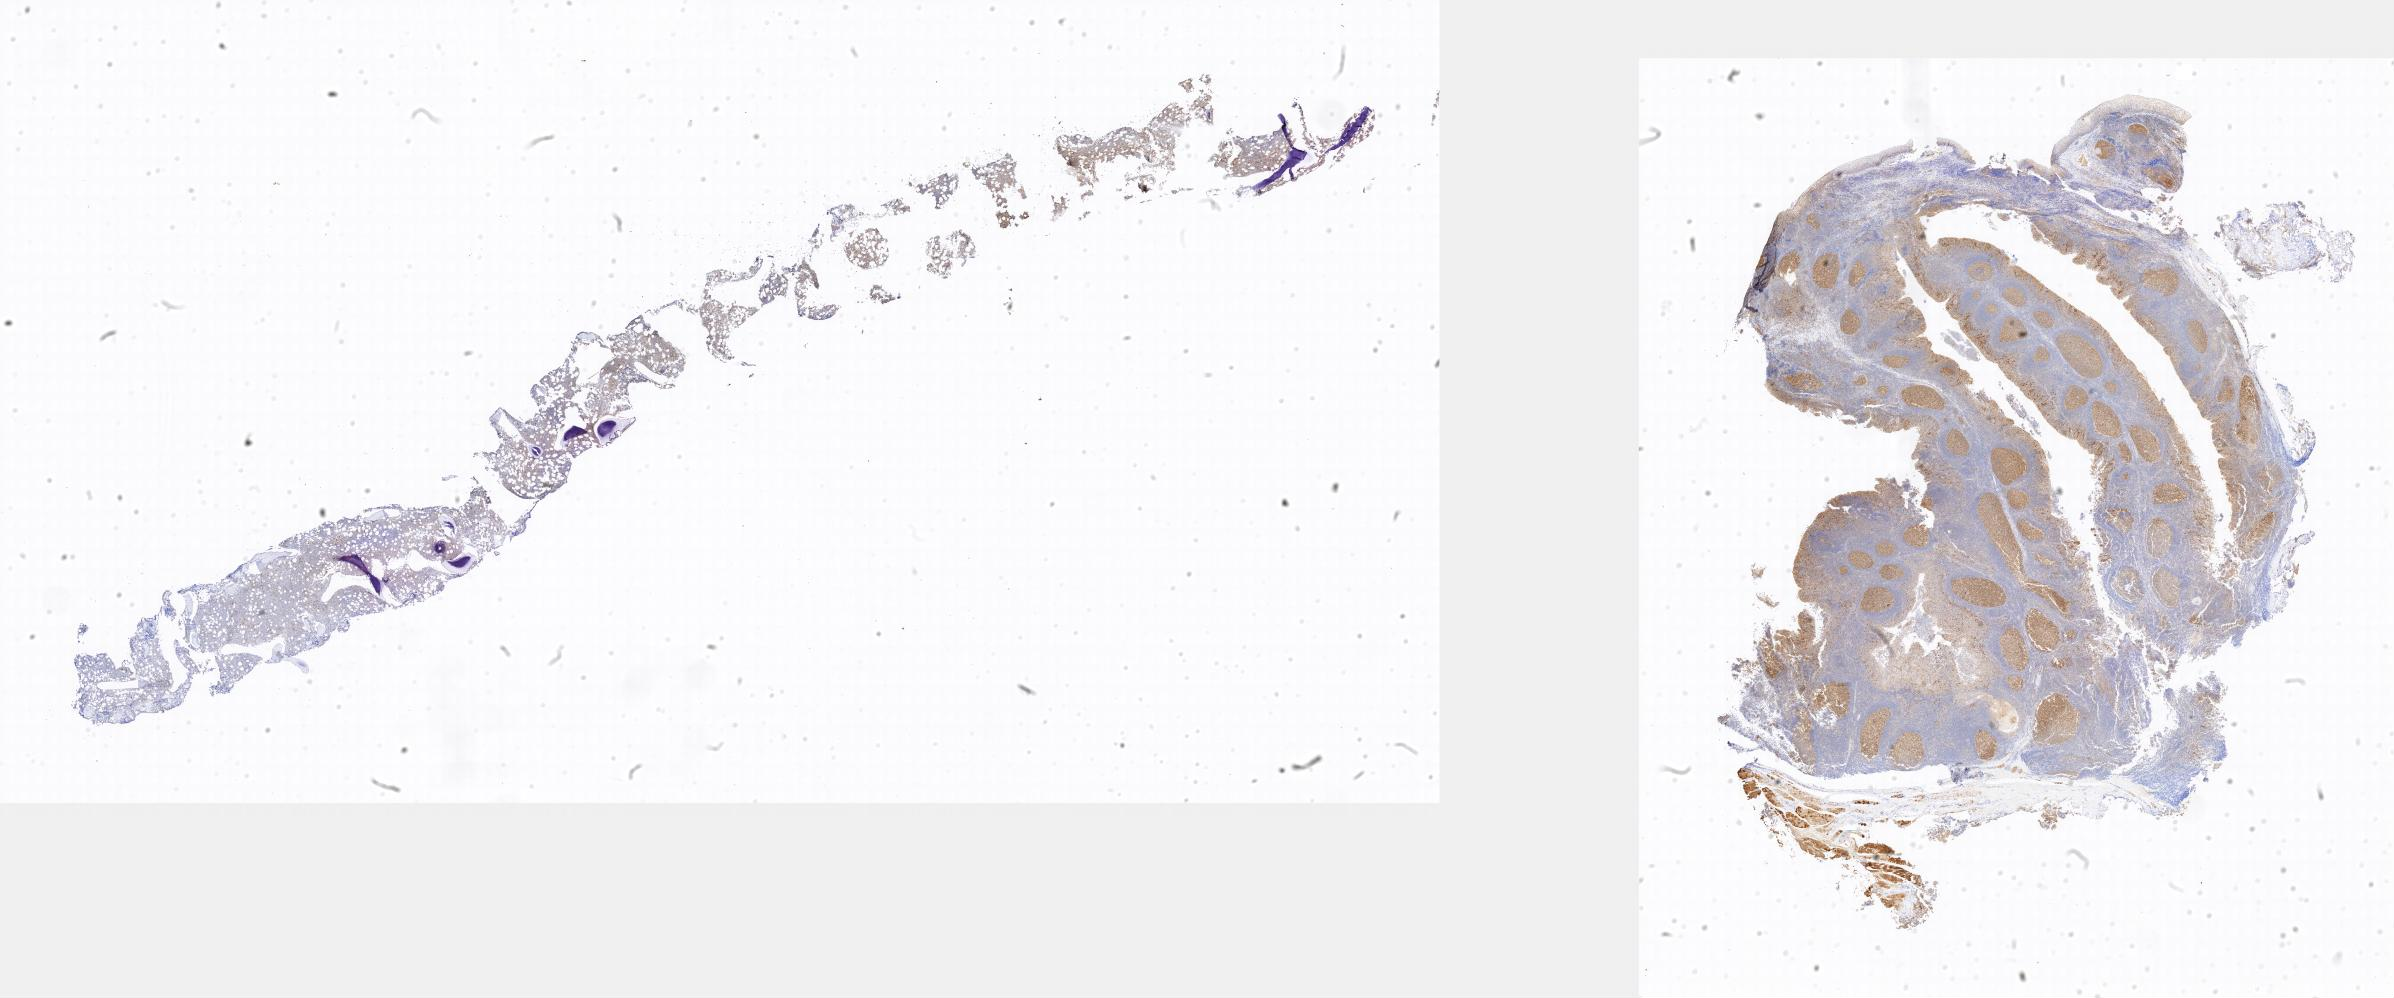
Whole-slide image, immunohistochemical stain for BCL6 — whole scanned area shown as a low-resolution overview. Specimen: tumor tissue. Site: bone marrow. Patient: male, 20 years old.
- histologic diagnosis: Diffuse large B-cell lymphoma, NOS